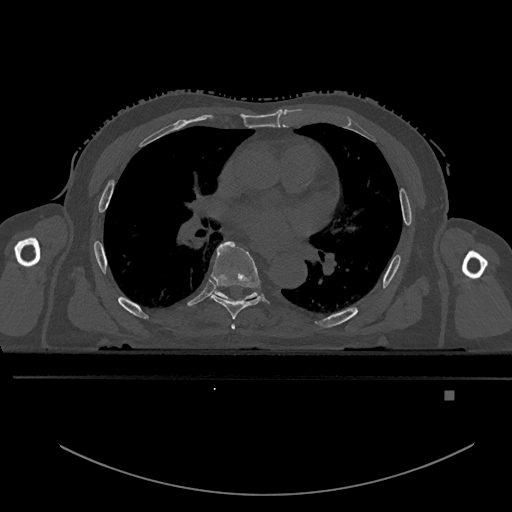
CT including the spine, one axial slice. Slice 294 of 969 in the series (ordered by position). Bone window (W 1800 / L 400 HU). 512 × 512 image matrix. Male patient, age 82 years. Case-level facts recorded for this patient, not image findings: primary cancer: prostate; vertebrae with lytic lesions (as recorded): T11, T9, T8, T2.
Annotated regions visible in this slice (semi-automatically segmented with operator editing):
- T5 vertebra: bounding box [x1, y1, x2, y2] px = [231, 324, 236, 330]
- T6 vertebra: [211, 241, 260, 319]
- T7 vertebra: [214, 291, 256, 299]